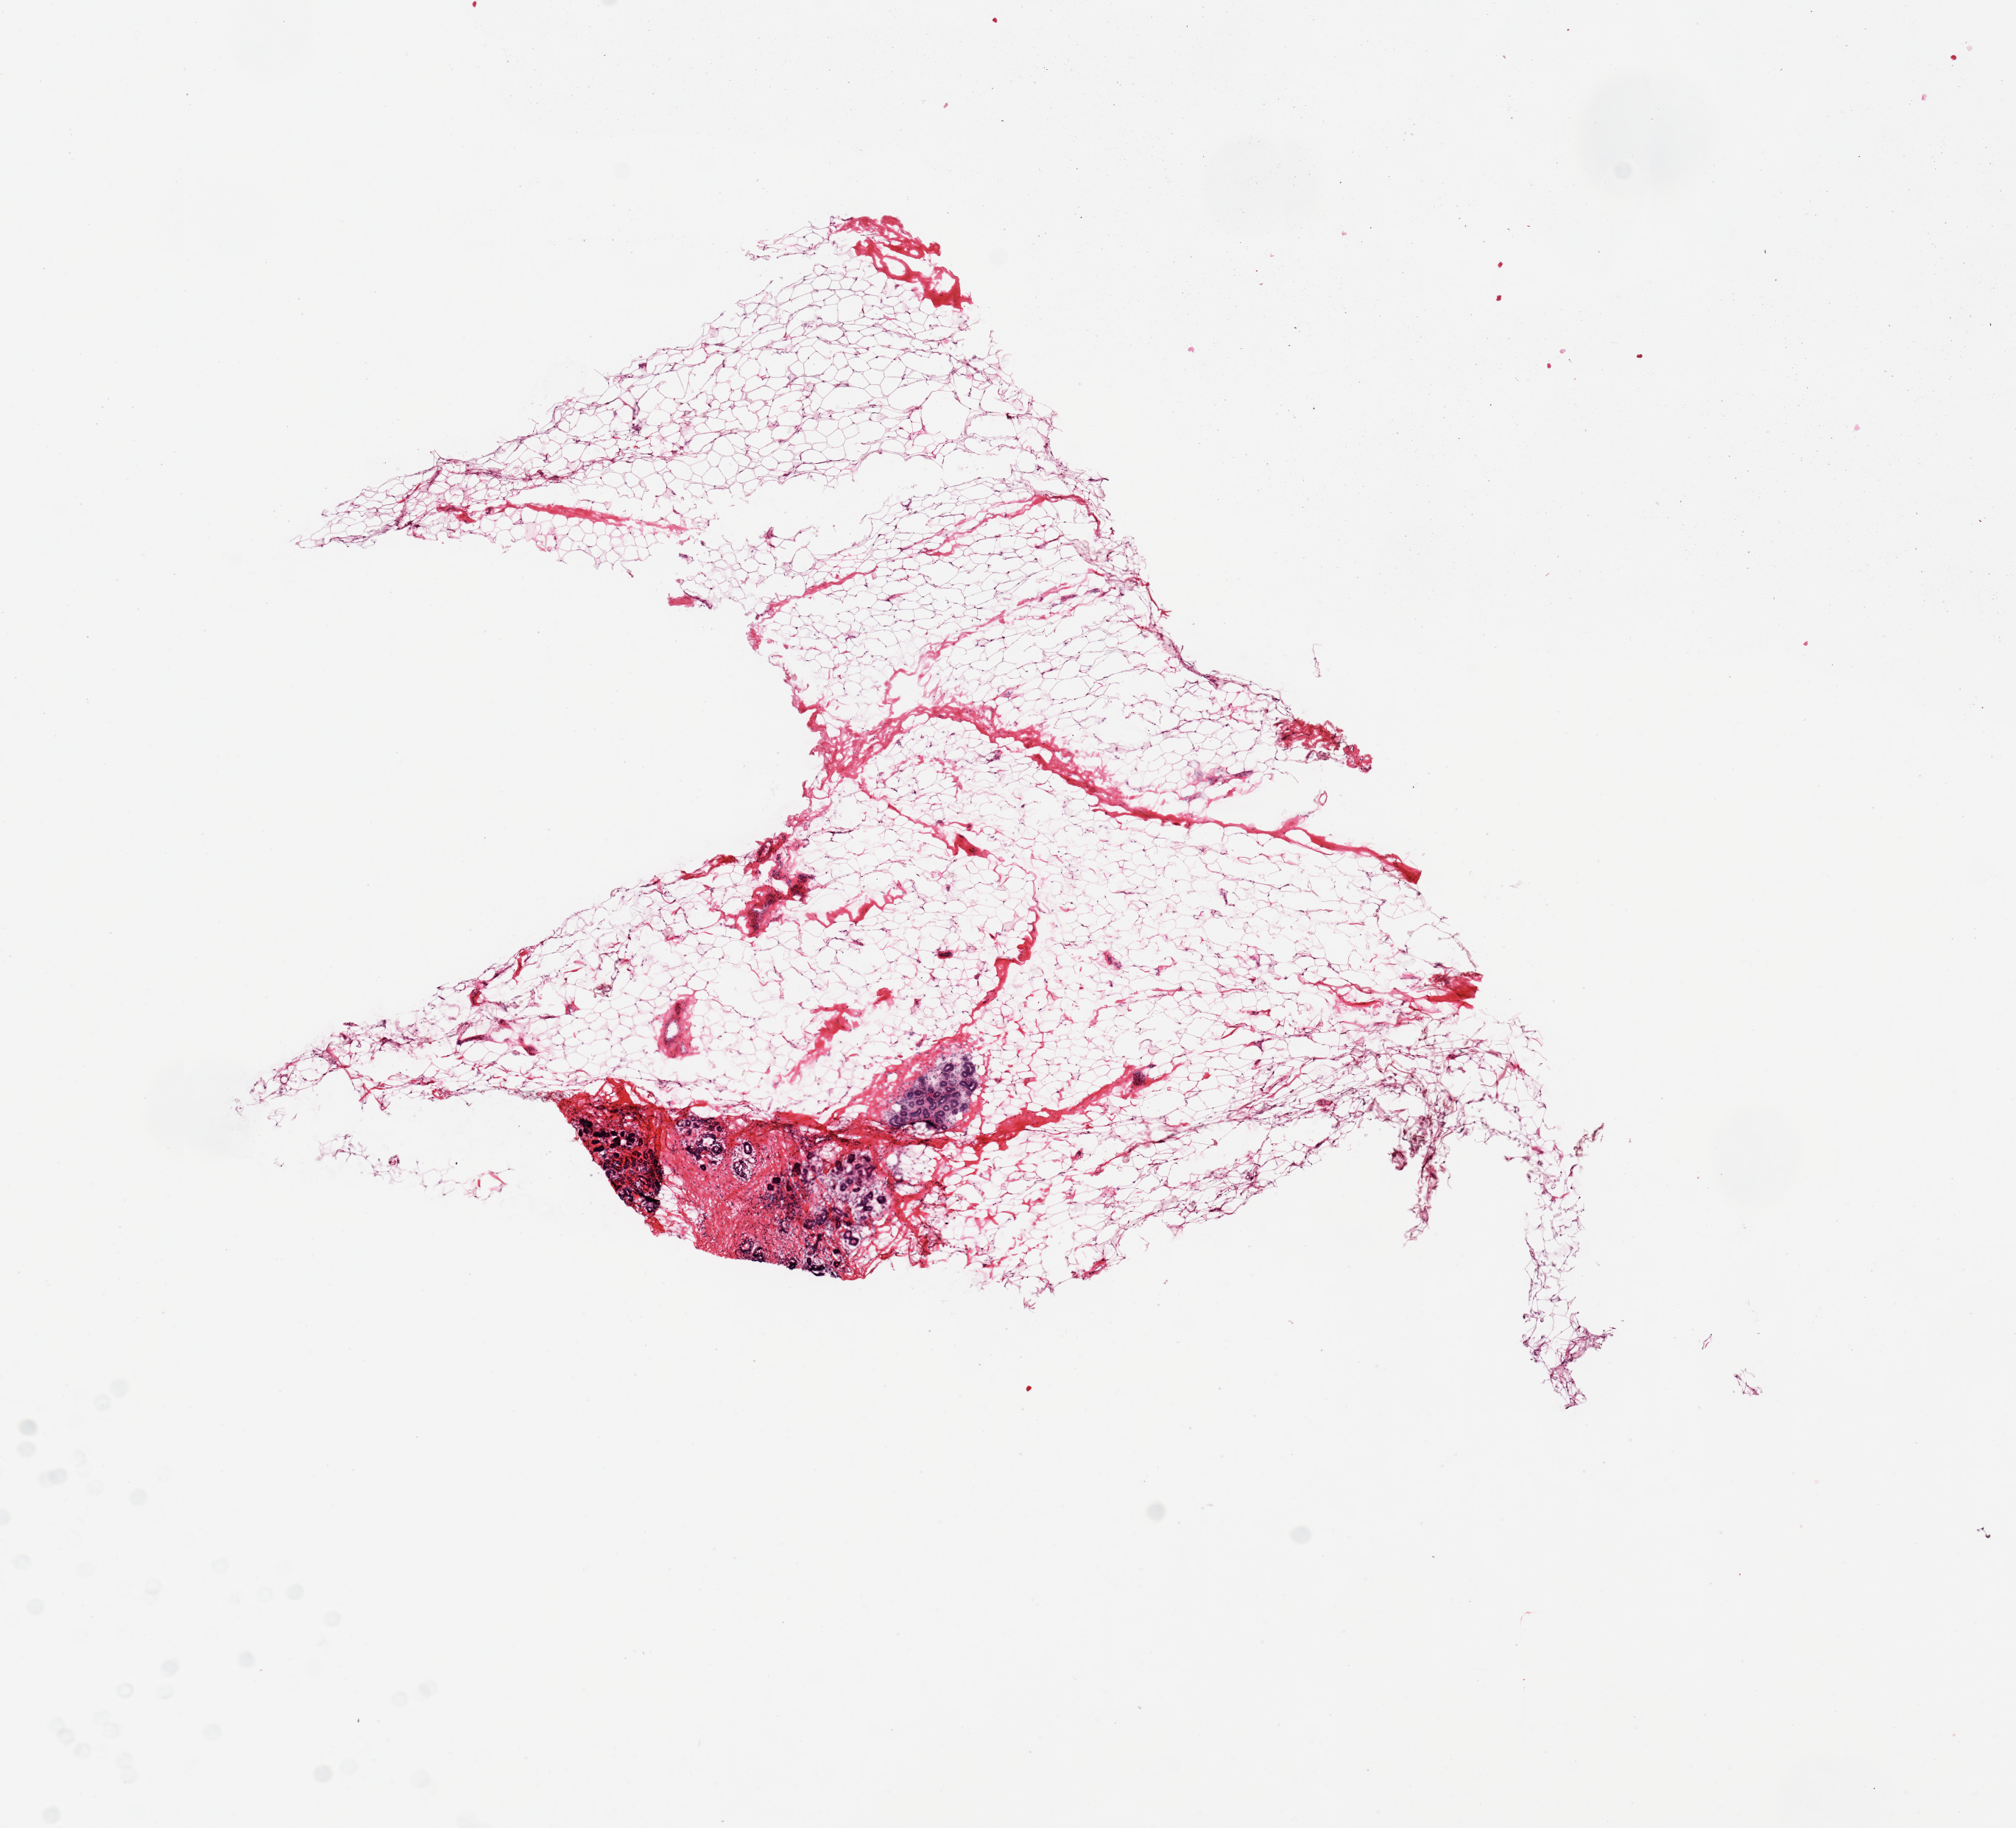
Hematoxylin and eosin (H&E) whole-slide image, a low-resolution overview of the entire scanned area, about 10.8 x 9.8 mm. Donor: female.
Specimen: frozen section (dry ice); target tissue: breast; tissue donor sample.